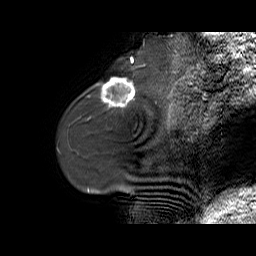
Breast MRI (dynamic contrast-enhanced), one sagittal slice; slice 17 of 70 in the series (ordered by position); dynamic contrast-enhanced series, time point 2 of 6 at this slice position (early post-contrast); 1.5 T; TE 5.5 ms, TR 32.9 ms; 4 mm slice thickness; 256 × 256 image matrix, field of view 240 × 240 mm. Female patient. Case-level facts recorded for this patient, not image findings: setting: breast cancer imaged before/during neoadjuvant chemotherapy; receptor status: HER2-positive.
Structures marked on this image (semi-automatic segmentation, software-assisted and operator-edited):
- analysis volume of interest (the breast-tissue region the enhancement analysis was run in; not a lesion): bounding box [x1, y1, x2, y2] px = [96, 73, 141, 110]
- tumour enhancement mask (voxels above the 100 % enhancement threshold inside the analysis volume of interest): [101, 78, 135, 106]